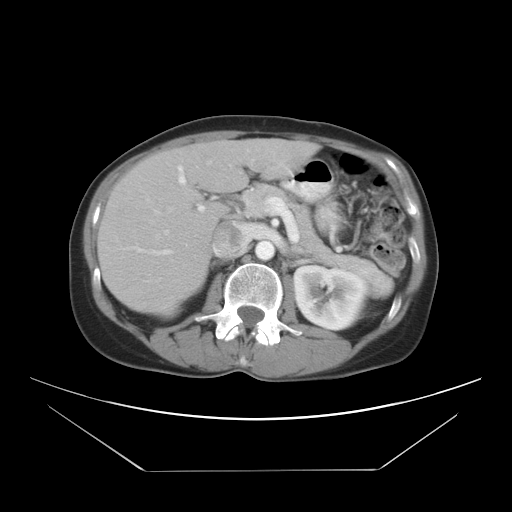
Contrast-enhanced abdominal CT, one axial slice; position 15 of 30 along the scan axis; 120 kVp; intravenous contrast given; soft-tissue window (W 400 / L 40 HU); 512 × 512 image matrix. Female patient, age 54 years. Case-level facts recorded for this patient, not image findings: diagnosis: colorectal cancer liver metastases, imaged before liver resection; multiple liver metastases: yes; largest metastasis: 2.5 cm; disease in both lobes: yes.
Structures marked on this image (manually delineated by an expert):
- hepatic veins: bounding box [x1, y1, x2, y2] px = [154, 210, 160, 214]
- liver: [101, 139, 312, 311]
- planned liver remnant (the part of the liver to remain after resection): [109, 141, 248, 311]
- portal vein (with intrahepatic branches): [123, 164, 206, 255]